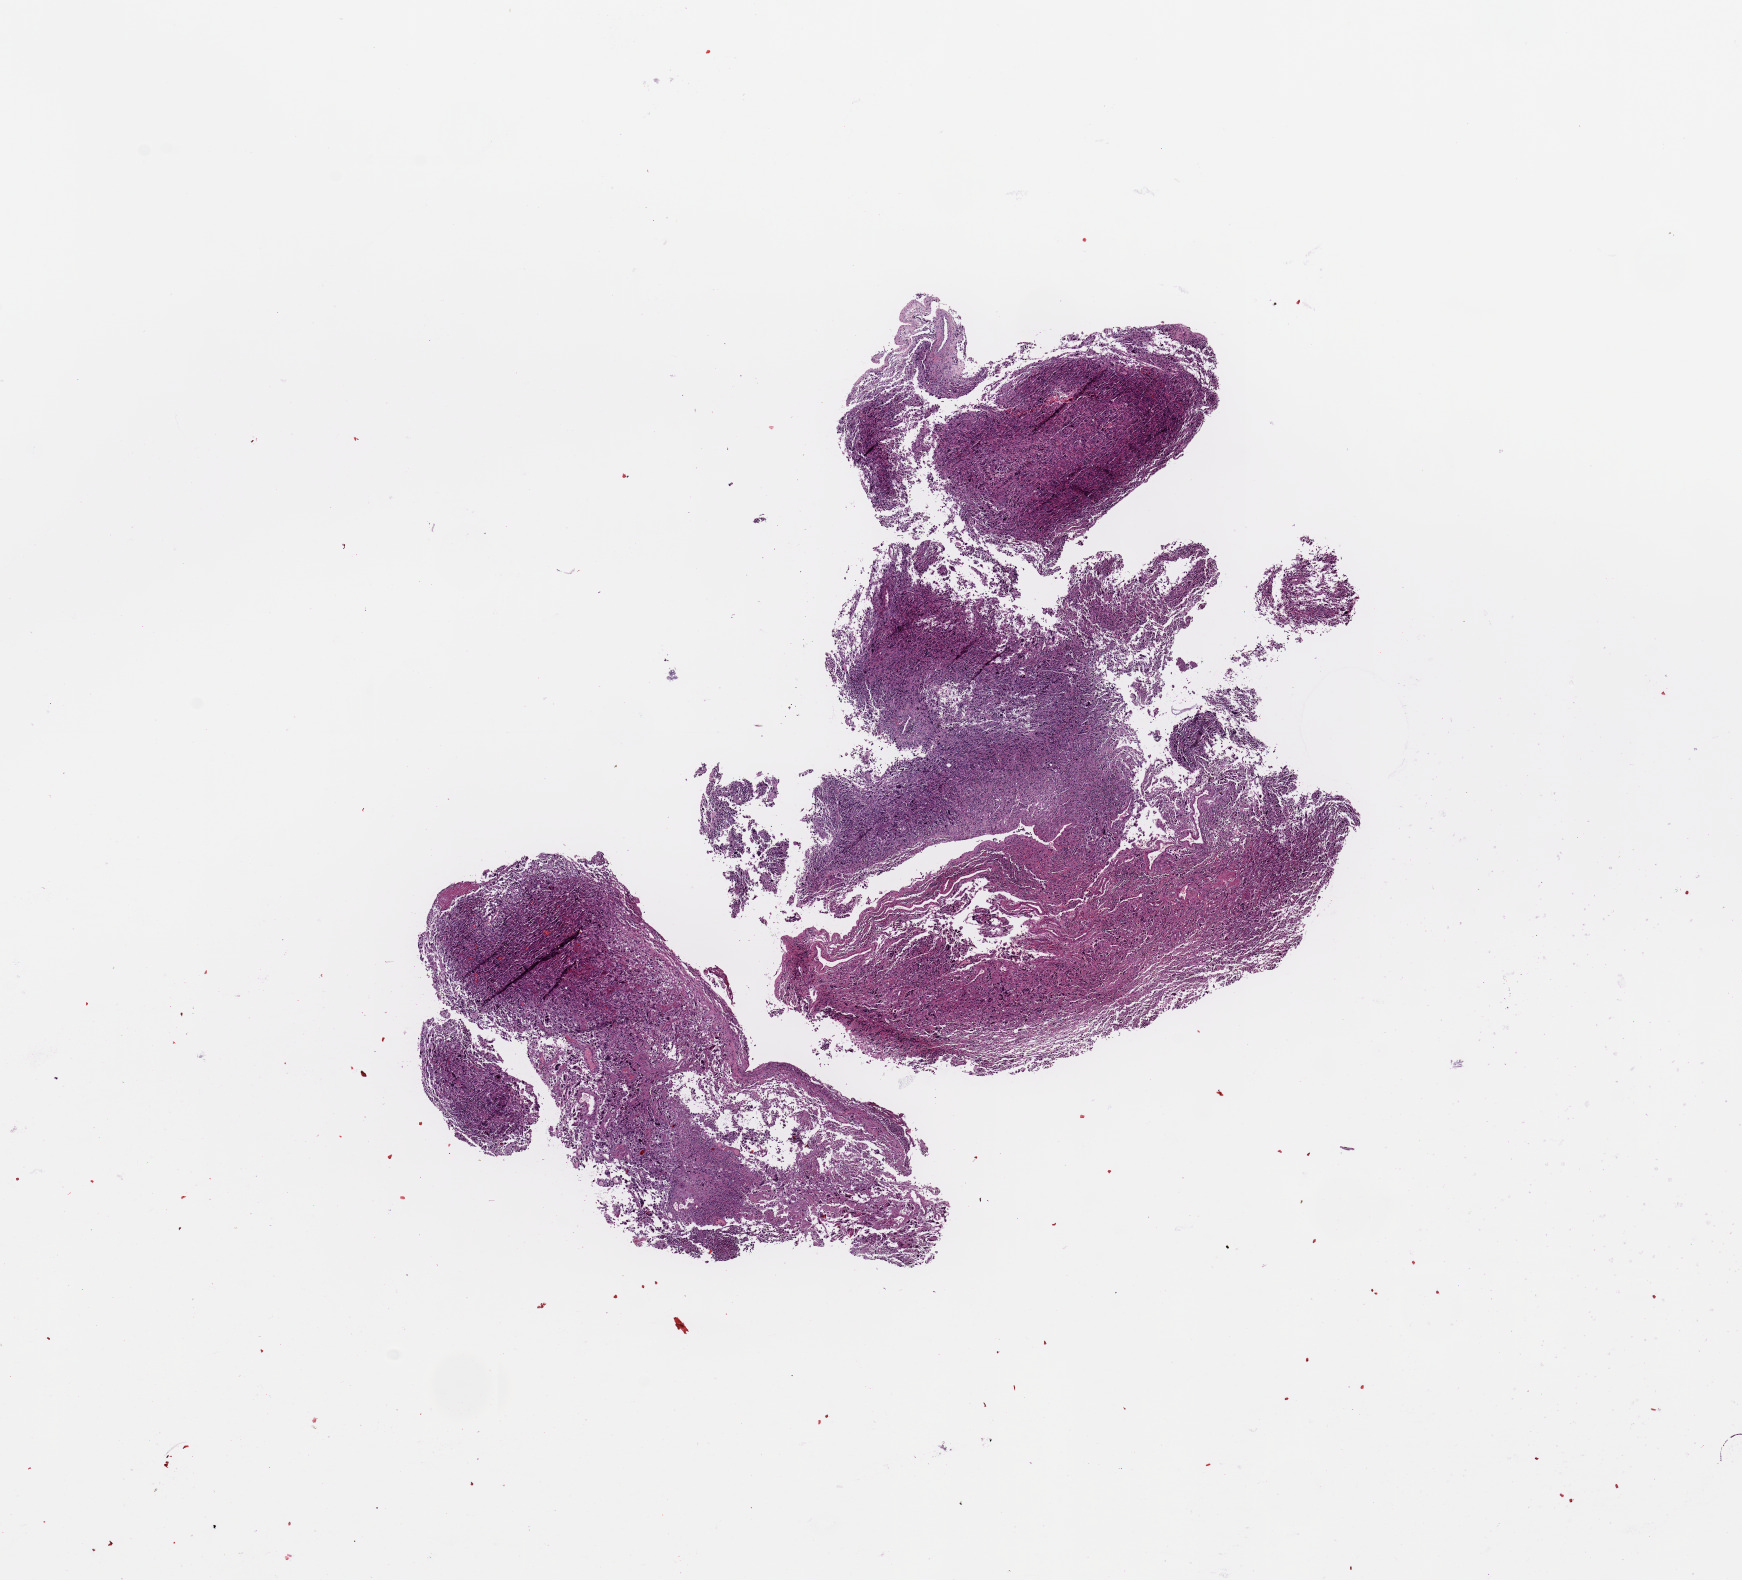
Digitized H&E-stained tissue section (whole slide) — a low-resolution overview of the entire scanned area, about 13.8 x 12.5 mm (acquisition: 20x scan); tumour tissue sample, sampled site: brain. Female, 39 y/o. Composition of this section per pathologist review: tumour nuclei 85%, necrosis 3%.
Diagnosis: Glioblastoma.